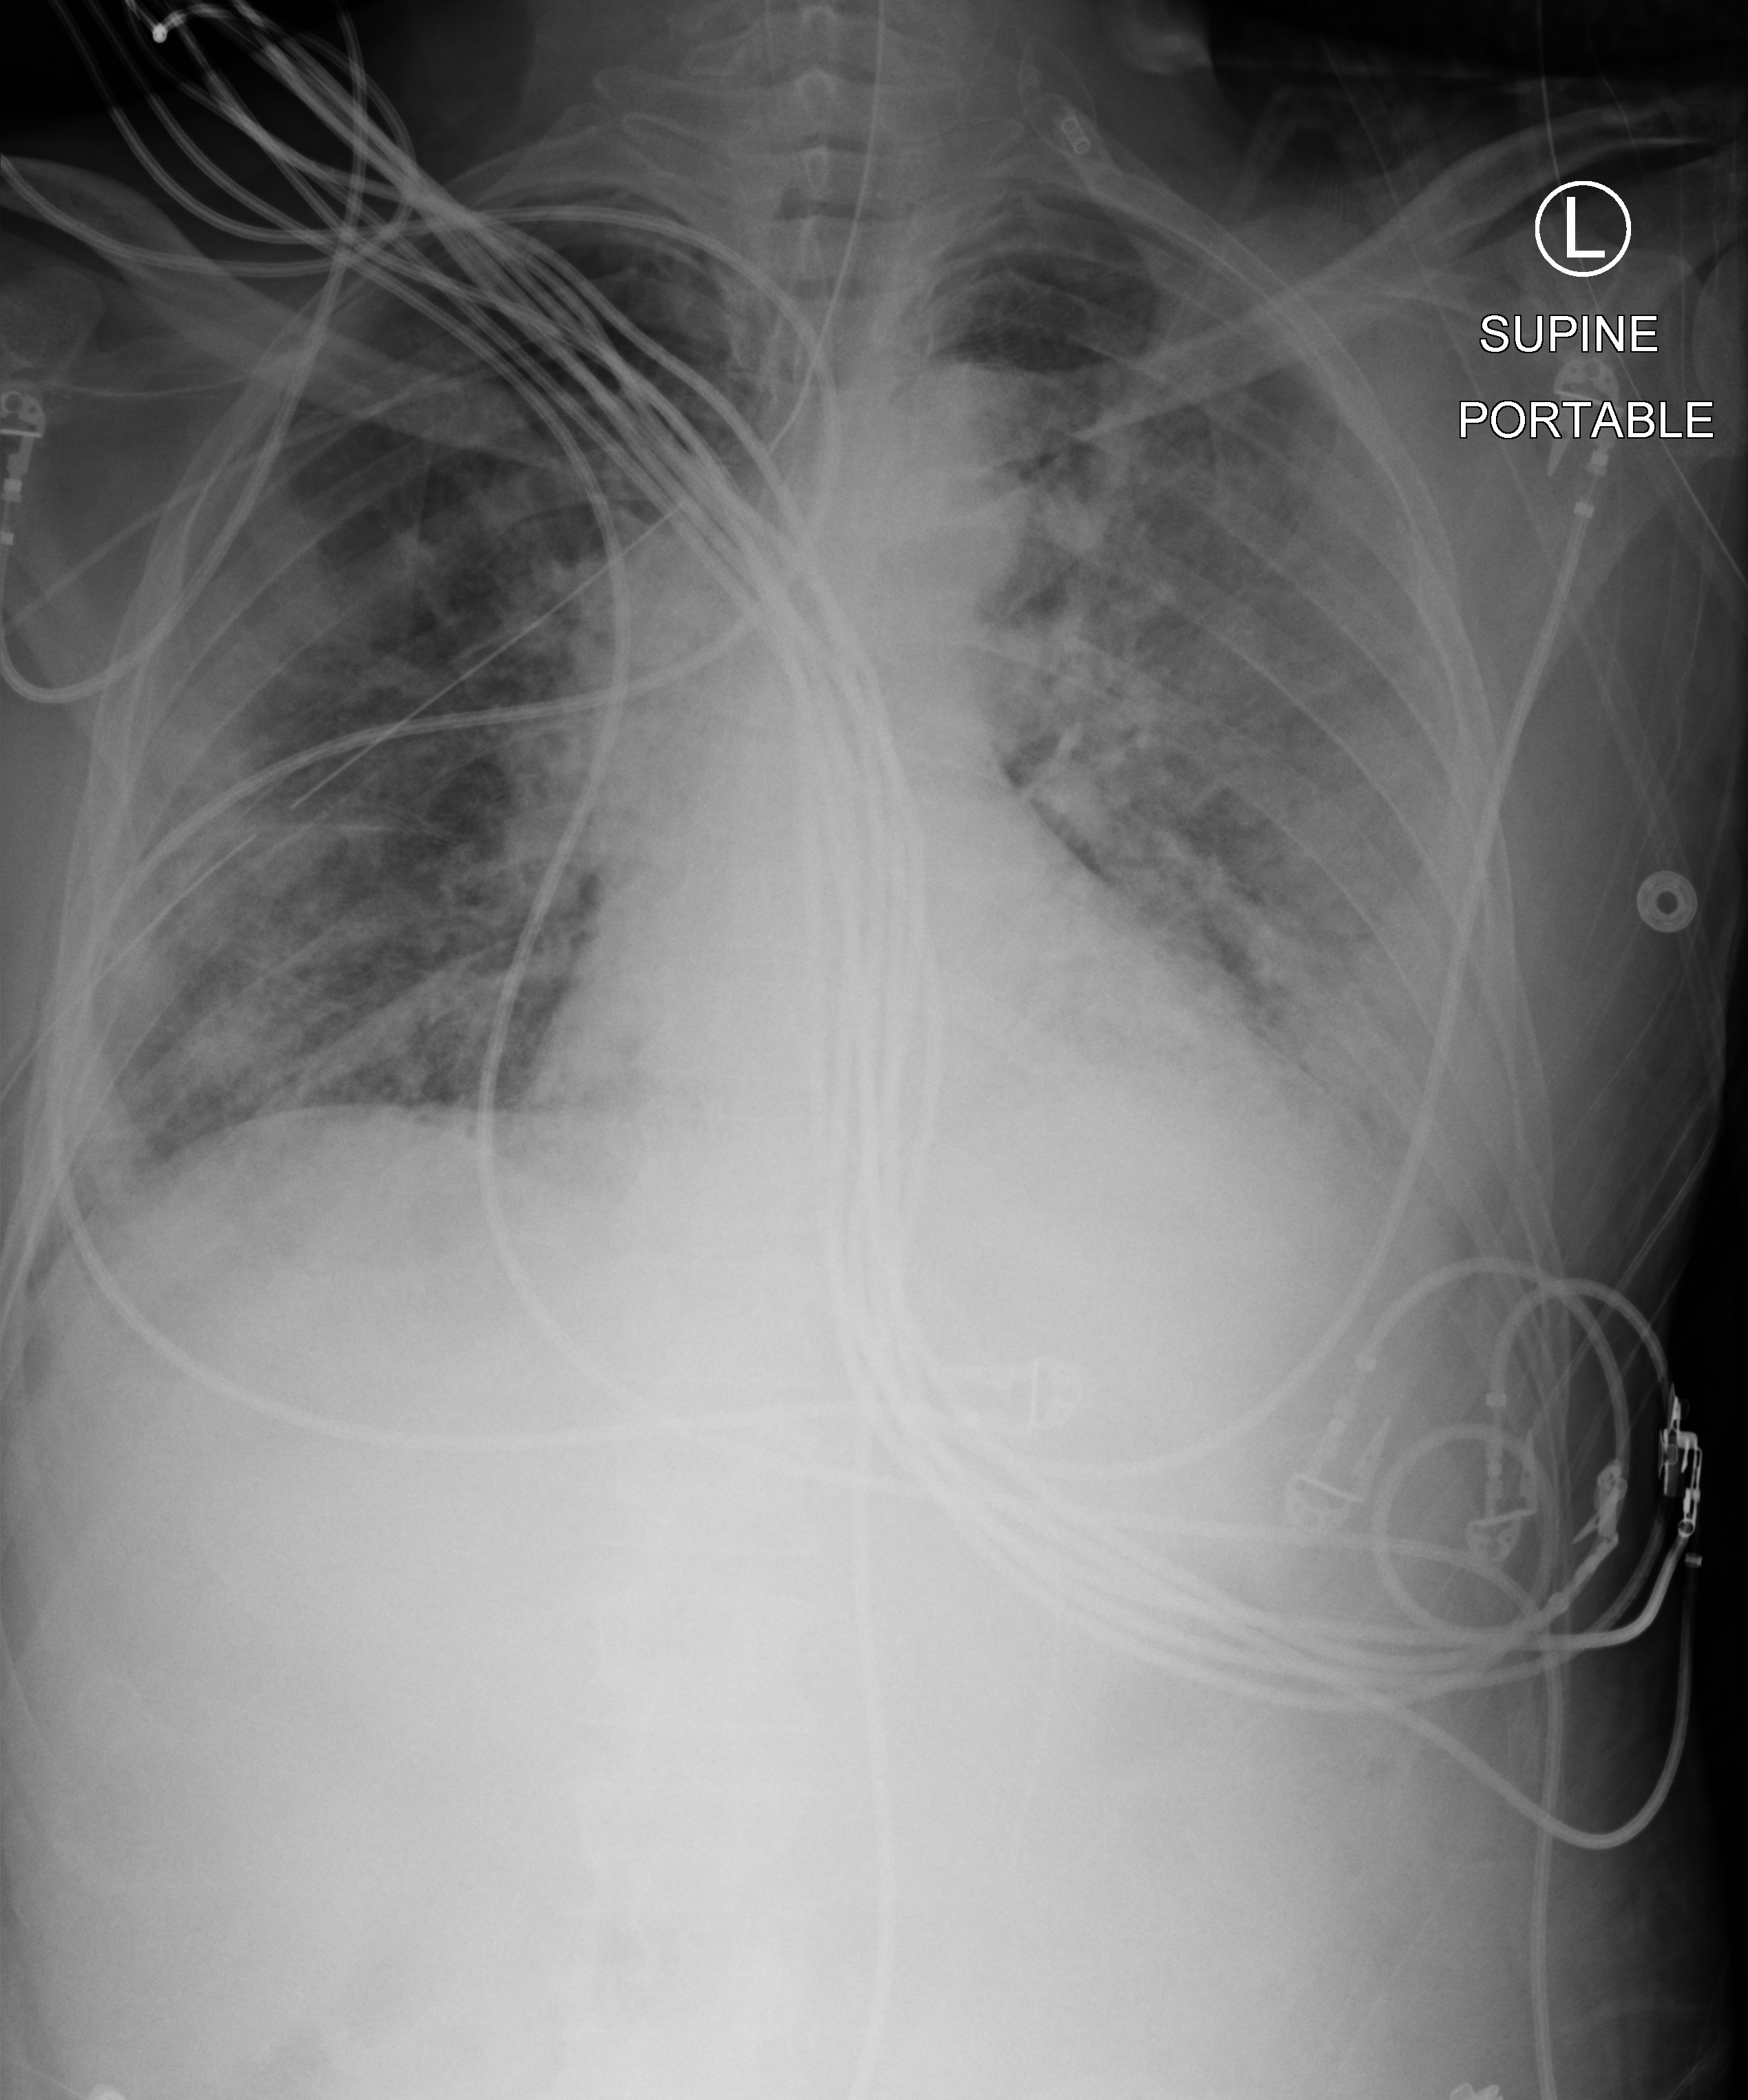
Portable chest radiograph. Patient hospitalised with COVID-19; male, aged 18–59 years.
From the hospital-stay record, not from the radiograph (when in the stay this image was taken is not recorded):
- other chronic lung disease (admission record): no
- chronic kidney disease (admission record): no
- diabetes (admission record): yes